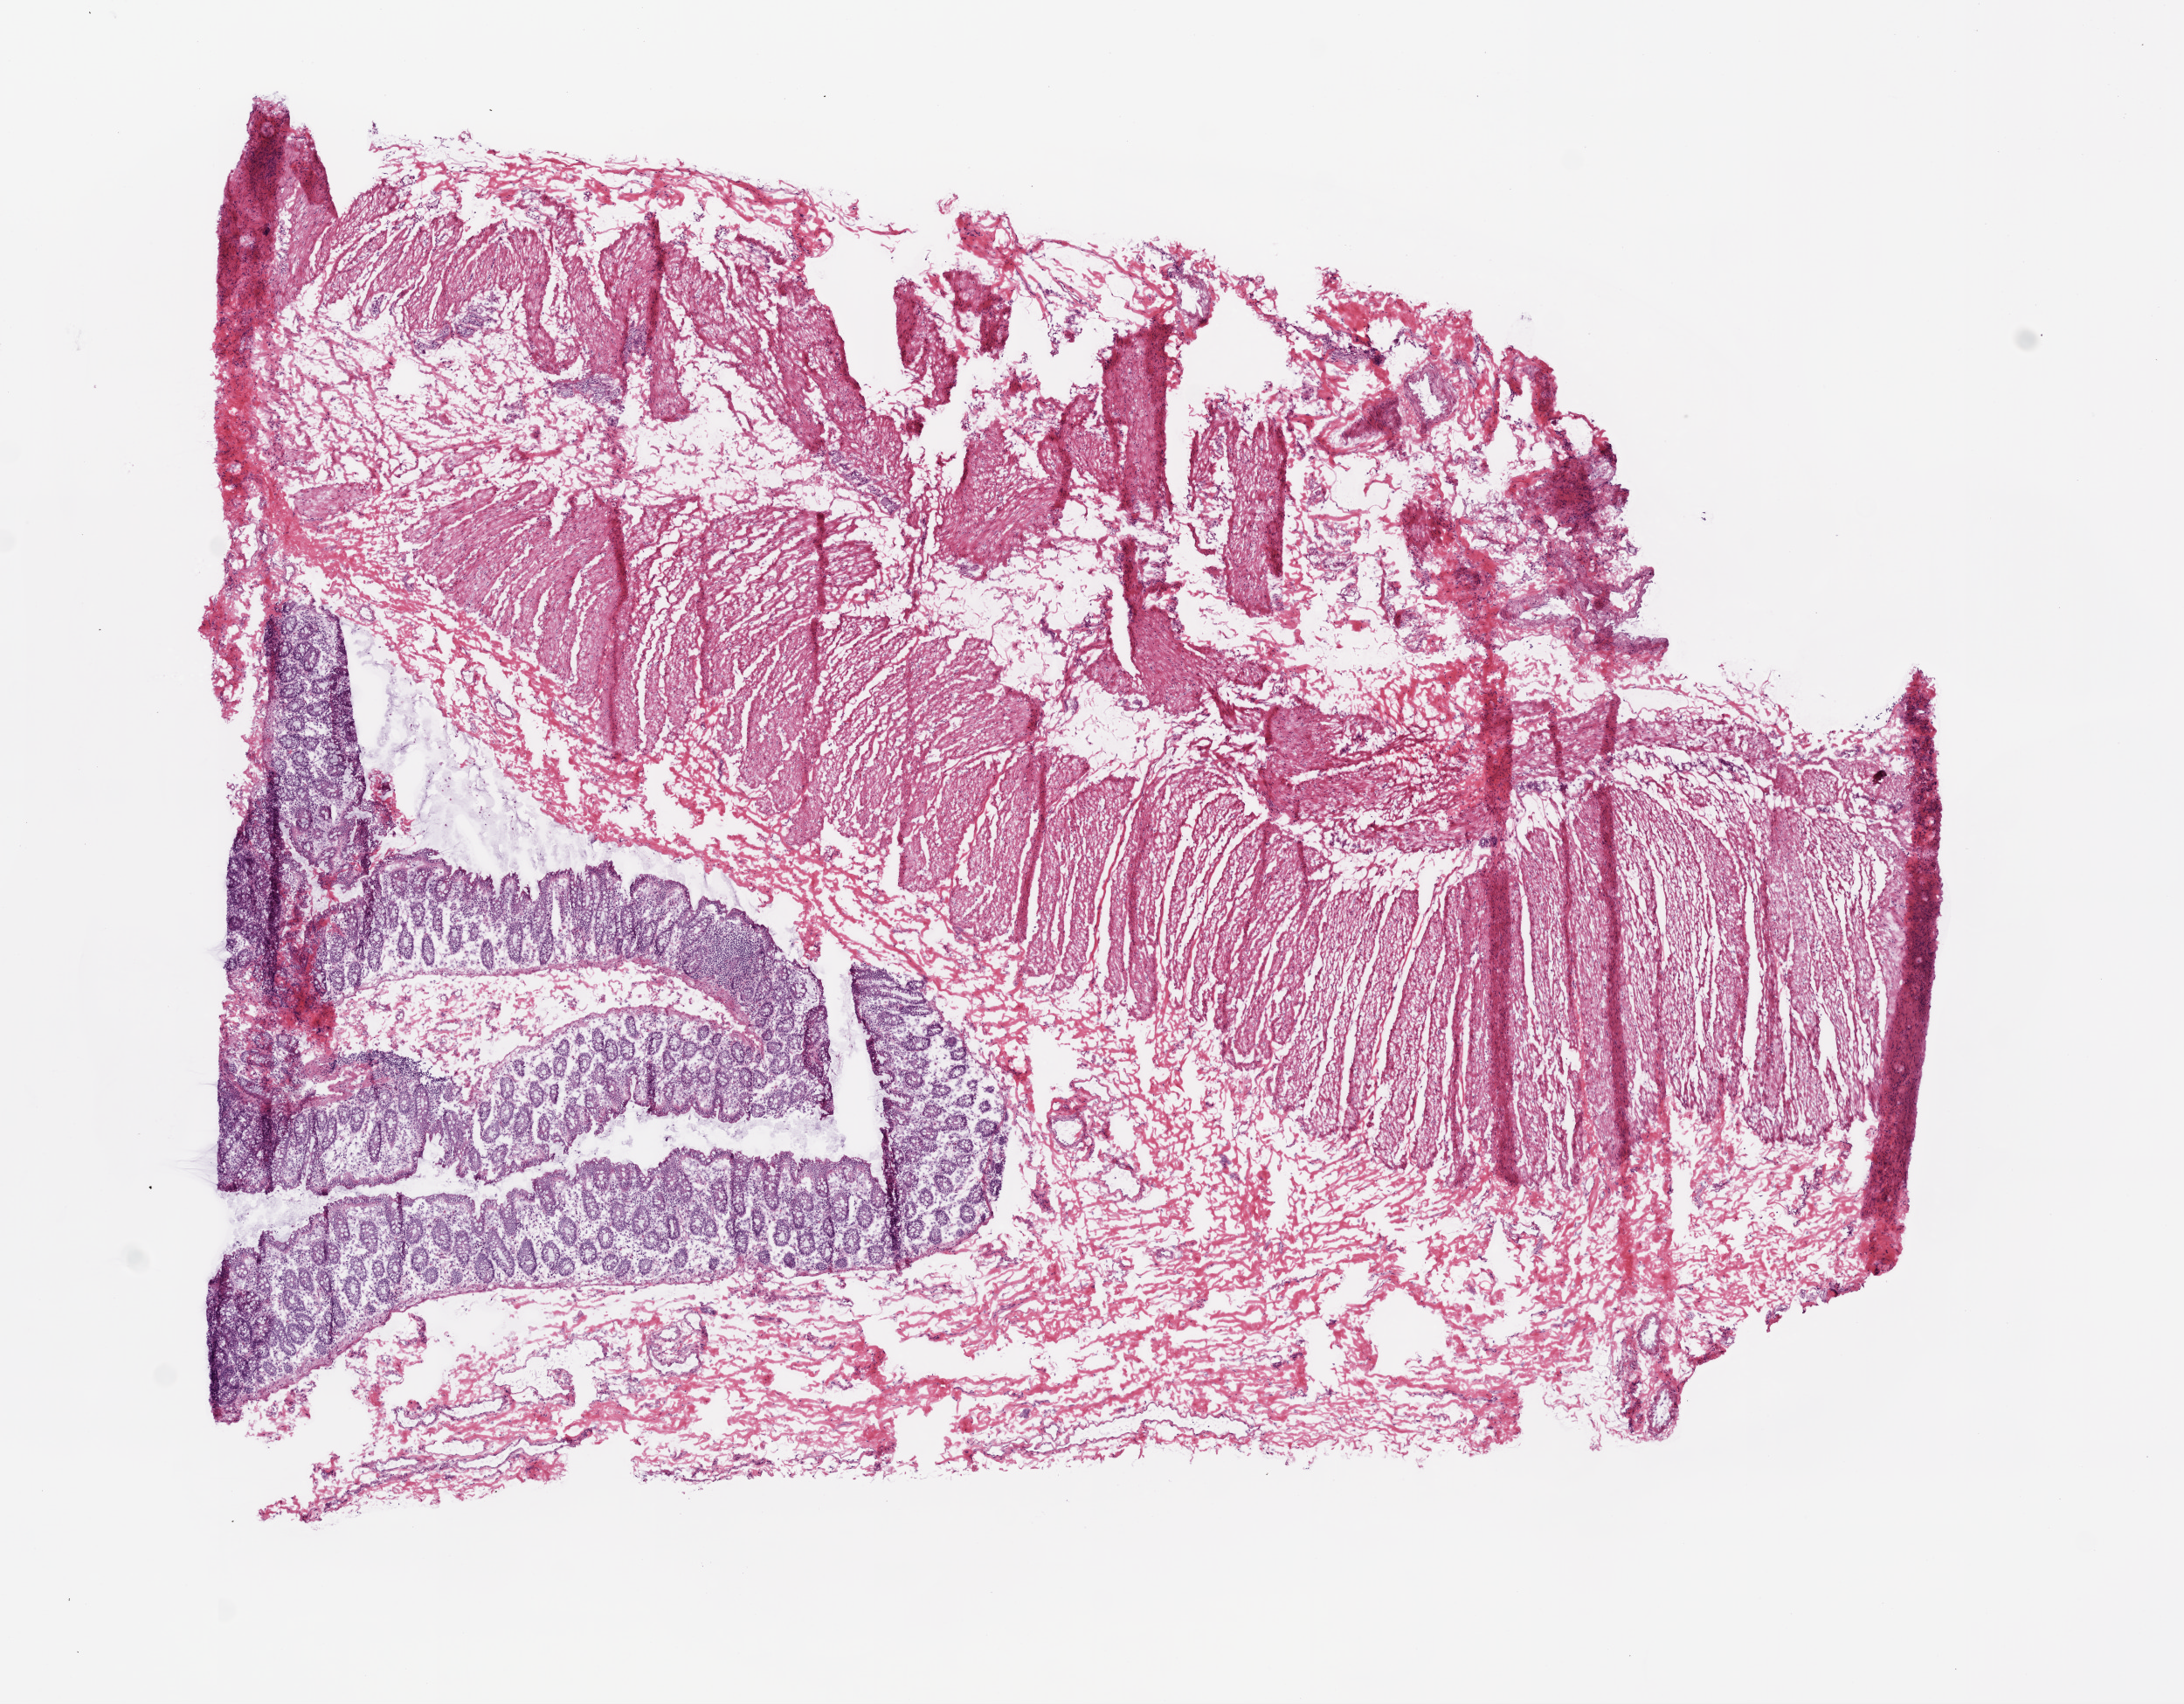
Whole-slide histology image, Hematoxylin and eosin (H&E) stained, shown as a low-resolution overview of the whole scanned area (about 10.0 x 7.8 mm), frozen section, colon, solid tissue normal (non-tumour tissue) sample. Patient: female, age at initial diagnosis 83 years.
This section: solid tissue normal (non-tumour) sample from the same patient. Patient diagnosis: Adenocarcinoma, NOS (ascending colon).